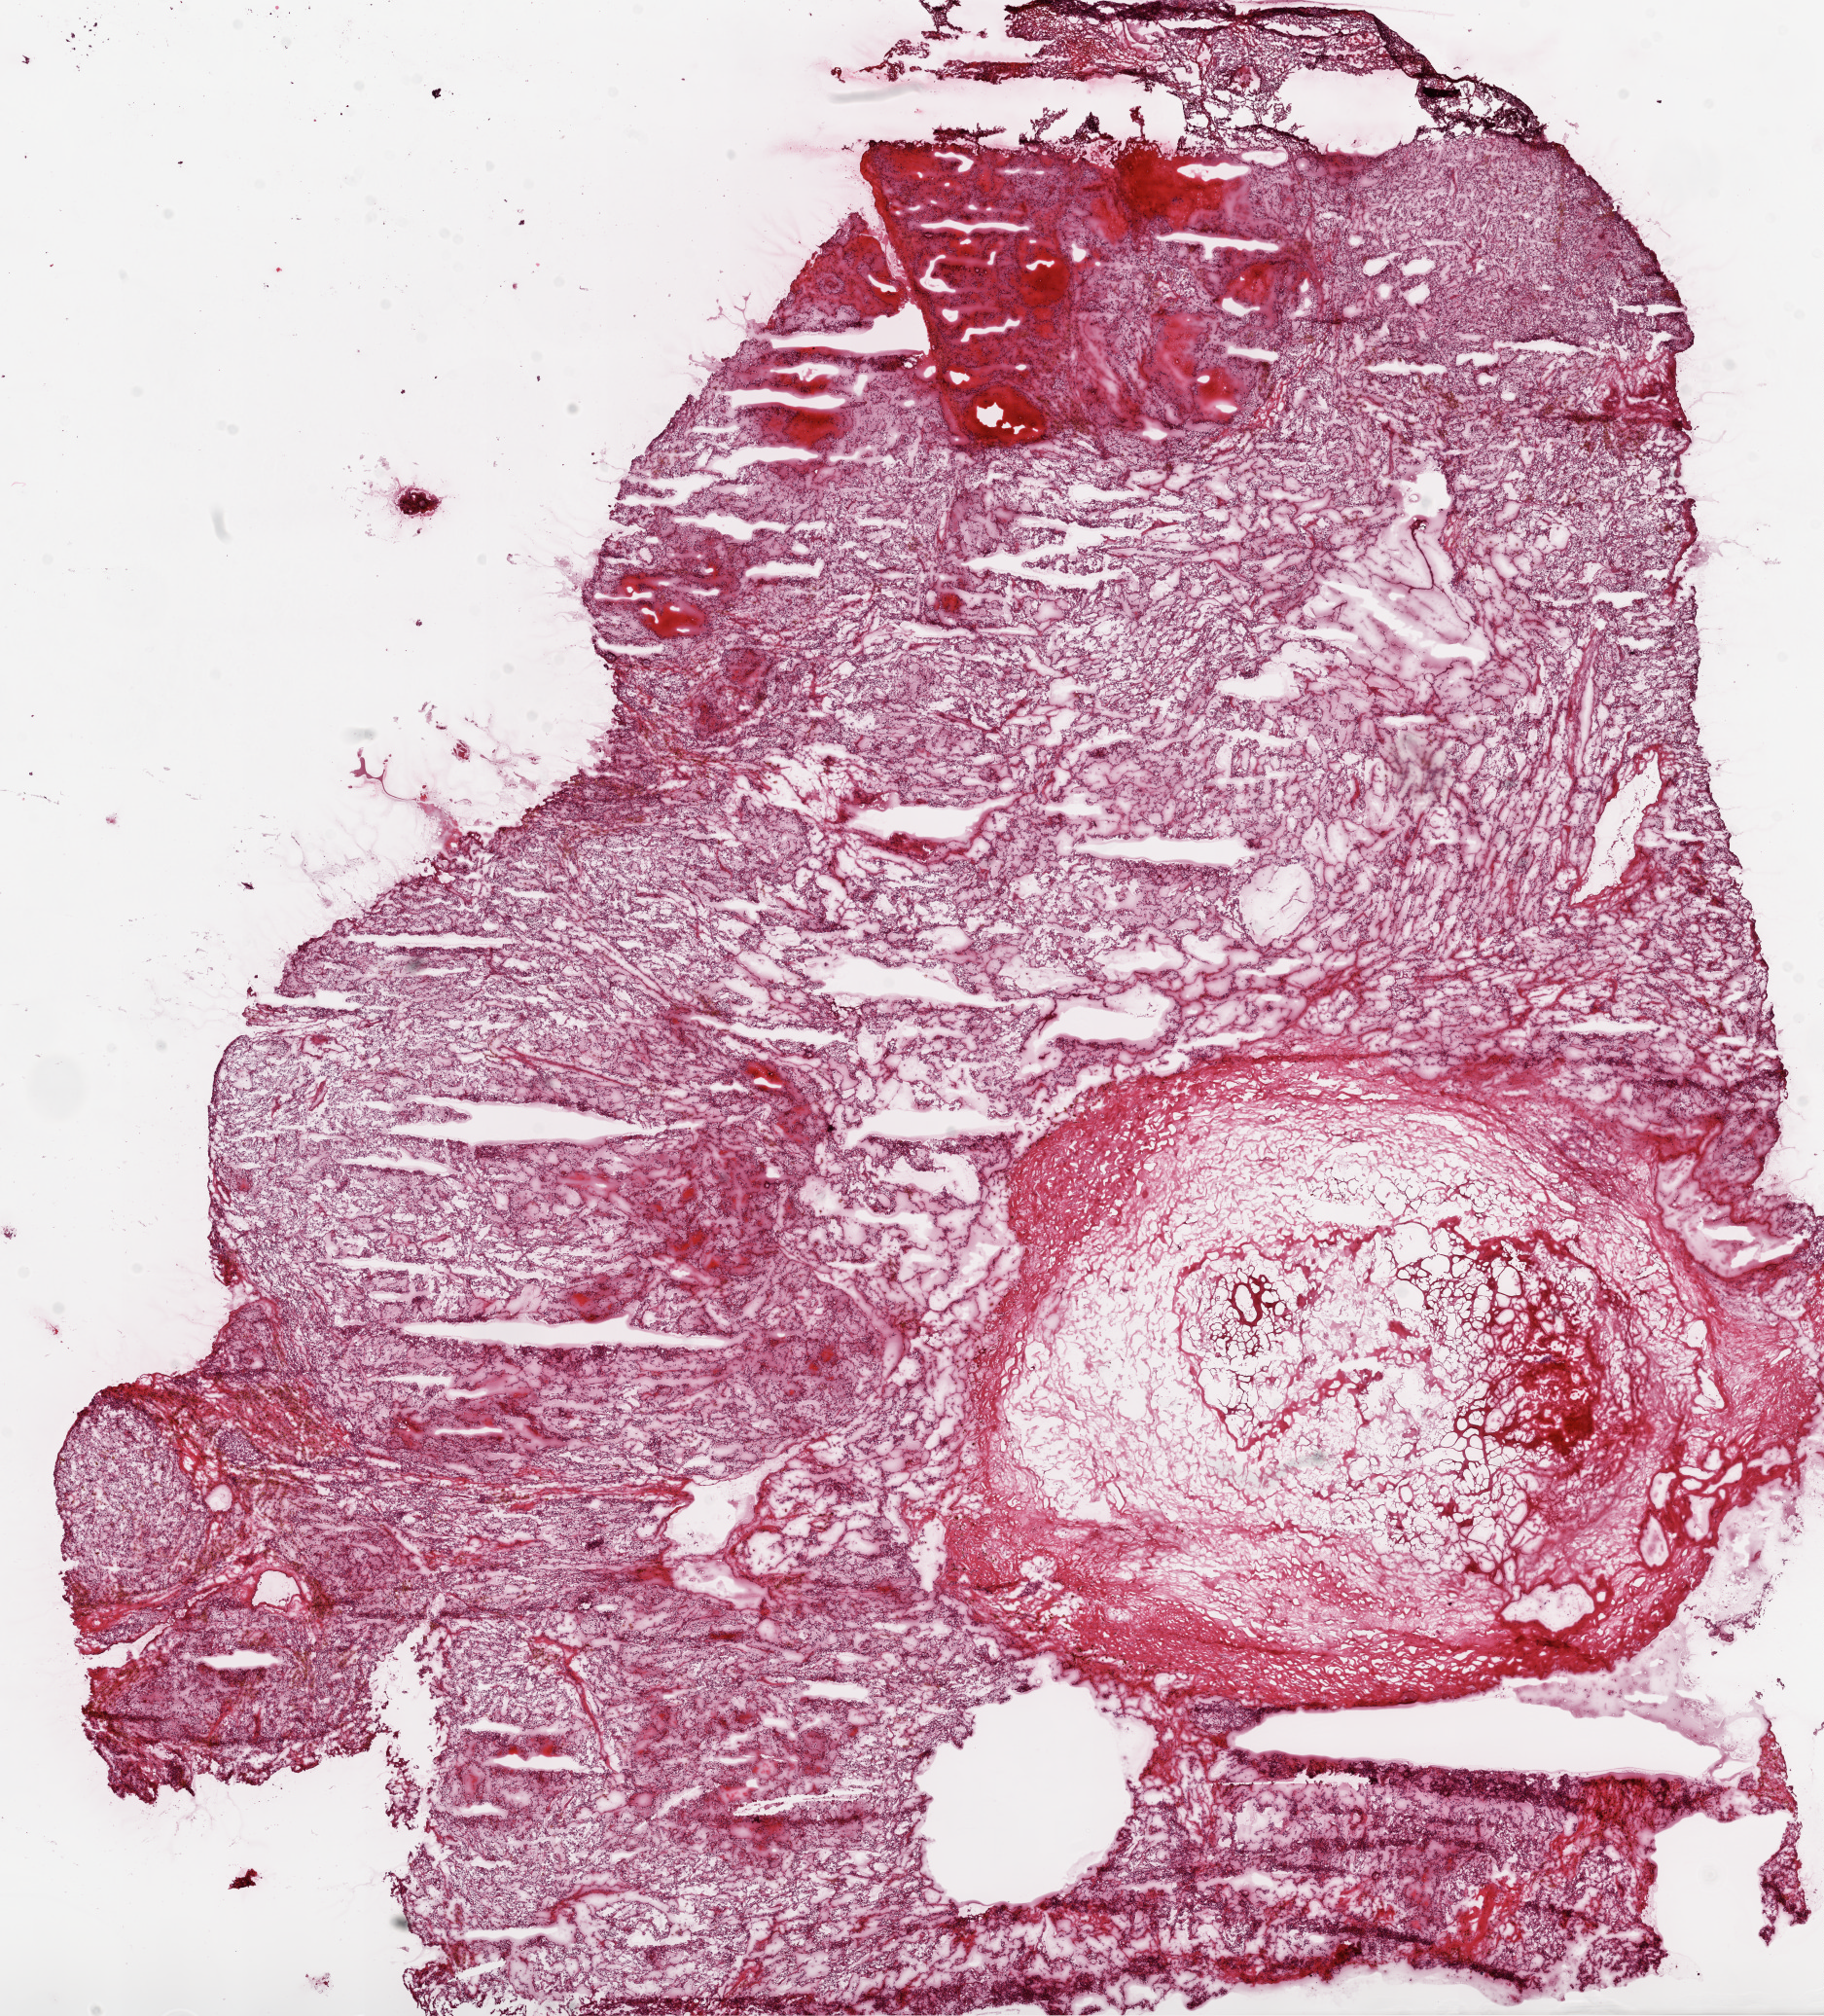
Digitized H&E tissue section (whole slide) — a low-resolution overview of the entire scanned area, about 15.0 x 16.6 mm (from a 20x scan); frozen section; sample: primary tumour, kidney. Male patient; age at initial diagnosis 55 years. Histologic grade: G2 (moderately differentiated). Pathologist review of this section (percent, as recorded): tumour cells 90%, tumour nuclei 80%, normal cells 0%, stromal cells 10%, necrosis 0%.
• laterality: right
• AJCC pathologic stage: I
• histologic diagnosis: Clear cell adenocarcinoma, NOS